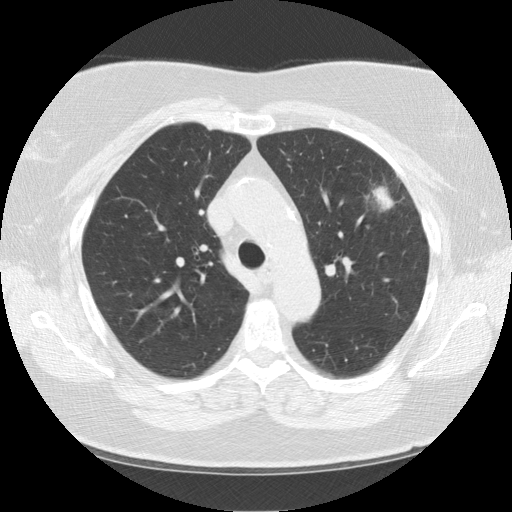
Low-dose screening chest CT, one axial slice; slice 93 of 130 in the series (ordered by position); lung window (W 1500 / L -600 HU); 2.5 mm slice thickness; 512 × 512 image matrix, field of view 350 × 350 mm.
Structures marked on this image (manually delineated by an expert):
- lesion 1 (tumor, upper lobe of left lung): bounding box [x1, y1, x2, y2] px = [372, 186, 394, 210]